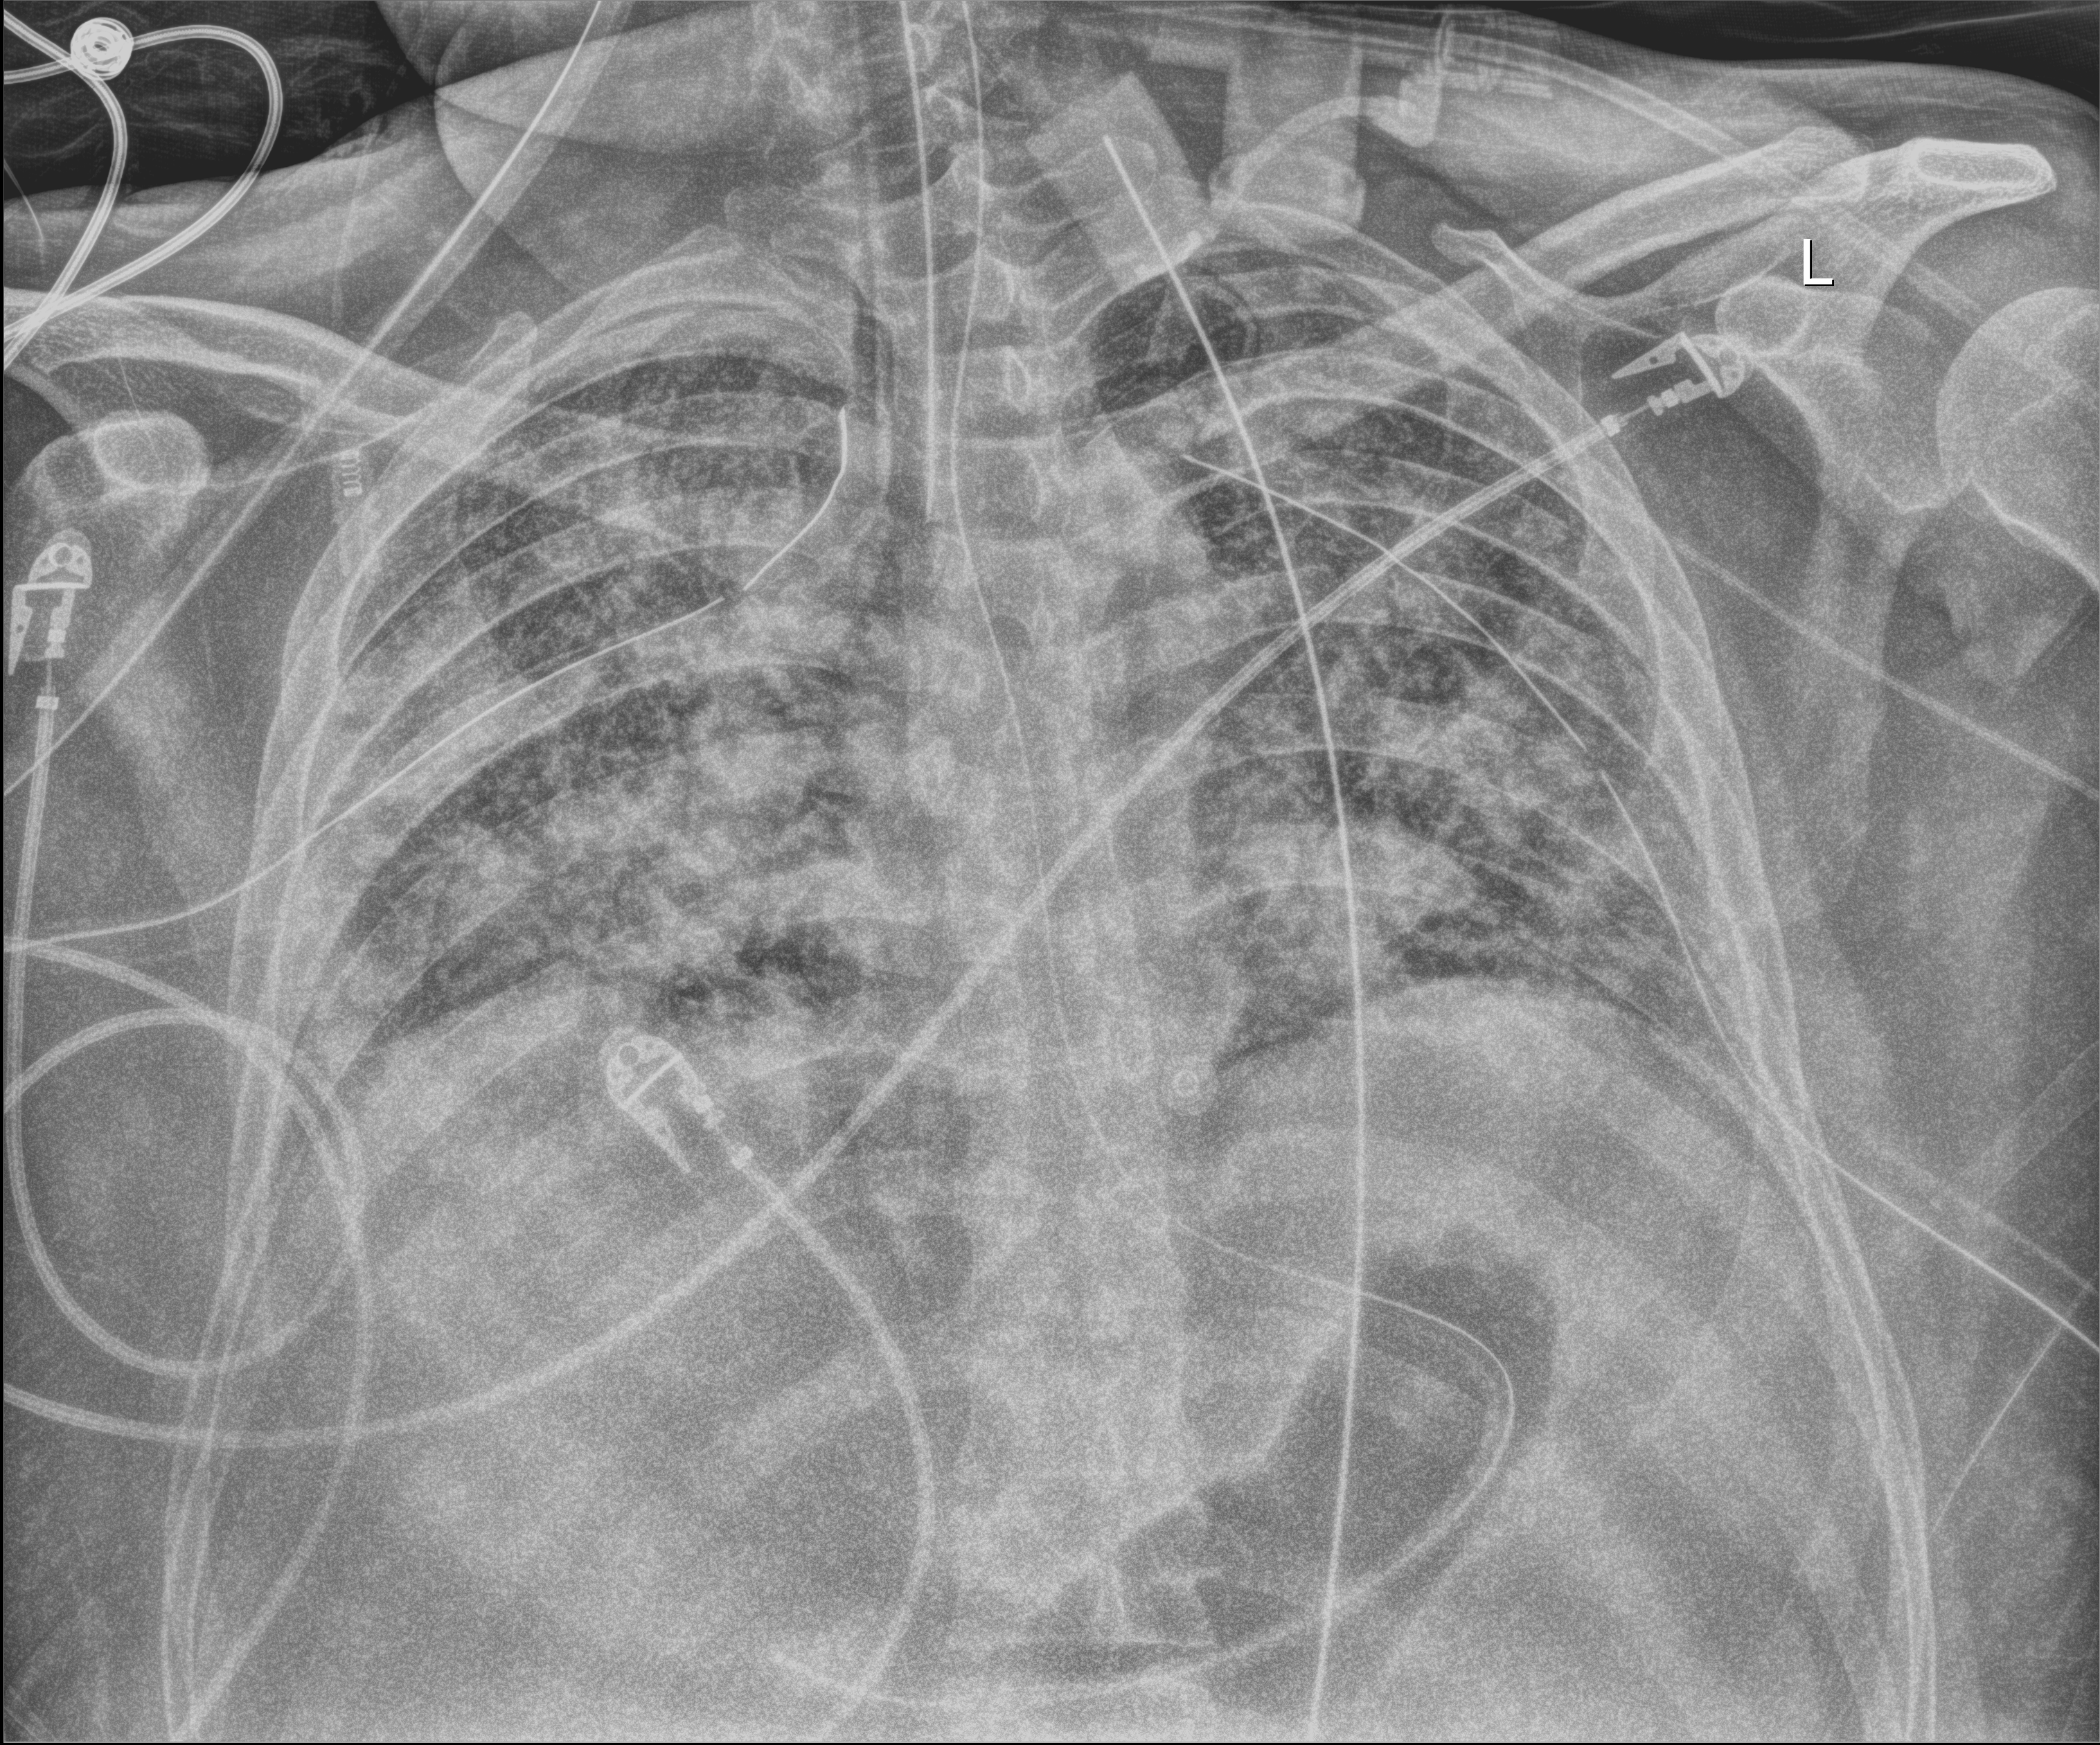
Portable chest radiograph, anteroposterior (AP) projection. Patient hospitalised with COVID-19; male, aged 18–59 years.
Admission-level facts for this patient (not findings on this image; timing relative to this image not recorded):
- mechanically ventilated during this hospital stay: yes
- diabetes (admission record): yes